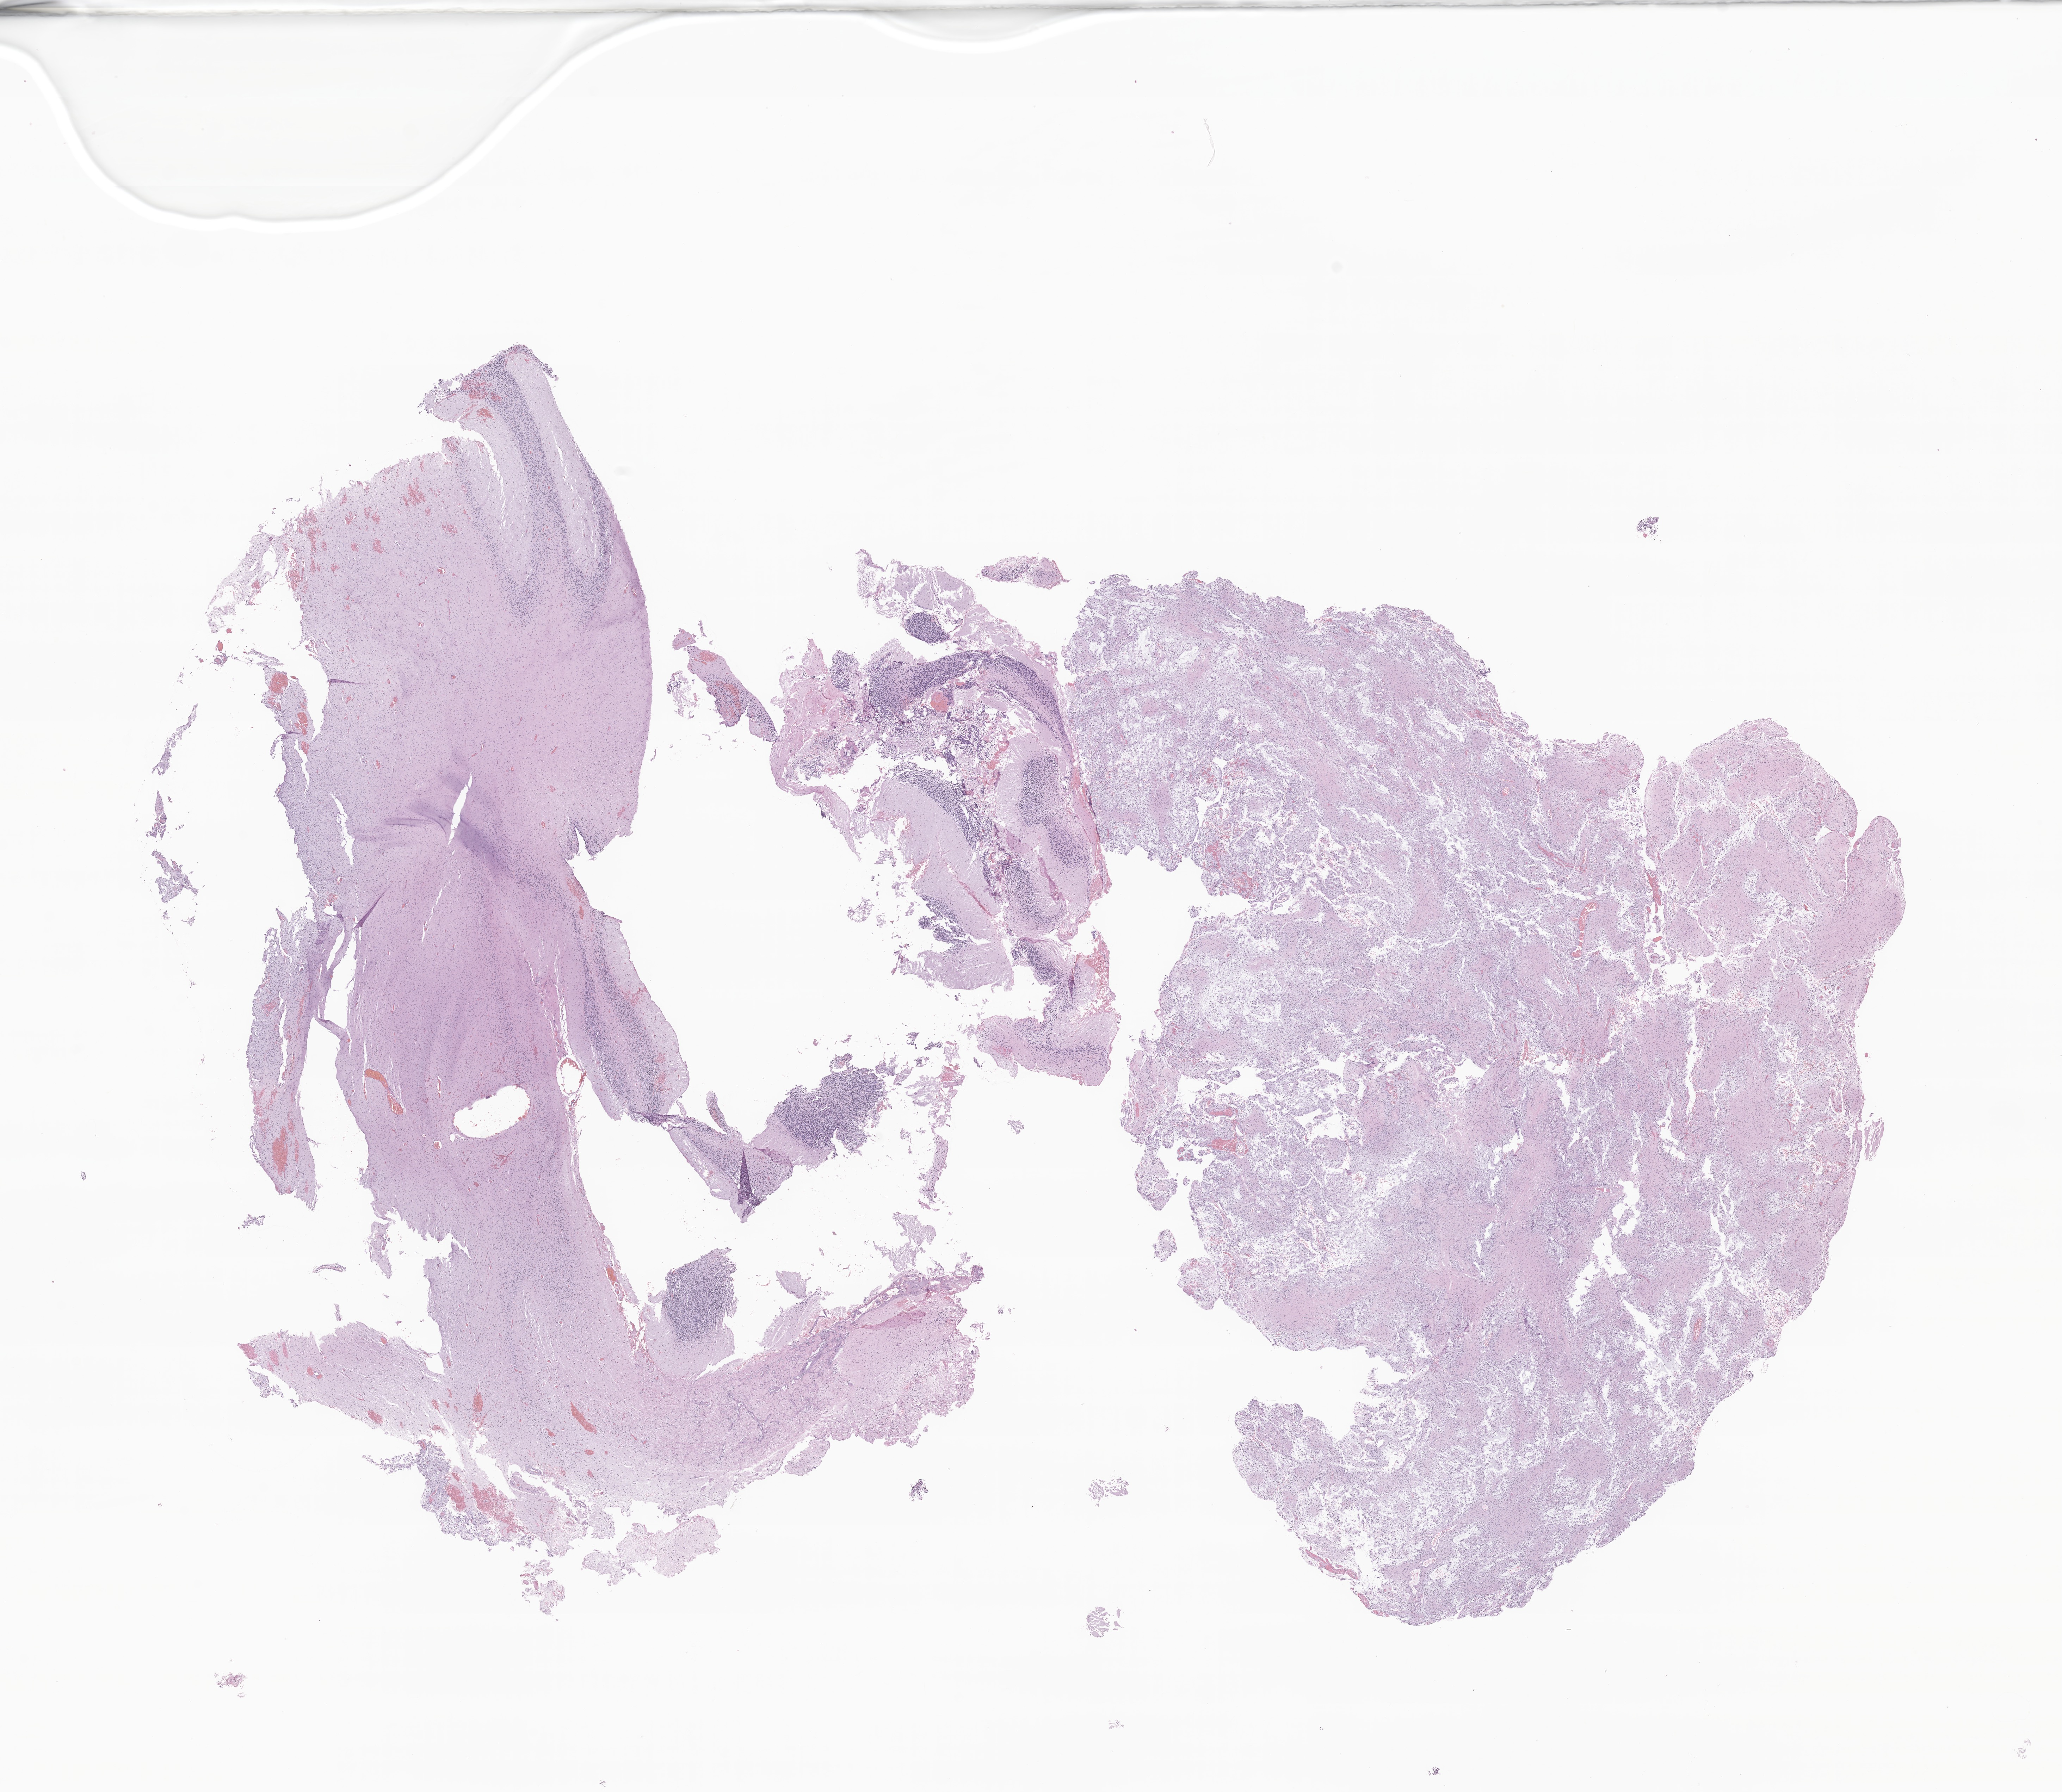
Whole-slide image, haematoxylin and eosin stain of tumor tissue from the cerebellum, low-resolution overview of the scanned area, about 24.7 x 21.4 mm; formalin-fixed, paraffin-embedded (FFPE) tissue. Female patient, age 115 months.
Diagnosis: Pilocytic astrocytoma.